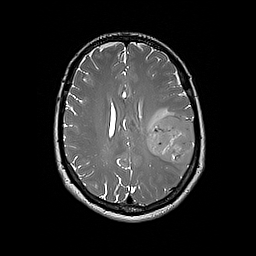
Brain MRI from a brain-tumour surgery series, one axial slice; slice 81 of 192 in the series (ordered by position); 1 mm slice thickness; 256 × 256 image matrix, field of view 250 × 250 mm. From the clinical record (not read from this slice): histopathology: Glioblastoma; WHO grade: 4.
Annotated regions visible in this slice (expert manual segmentation):
- tumour: bounding box (x1, y1, x2, y2) in pixels: (147, 115, 195, 165)